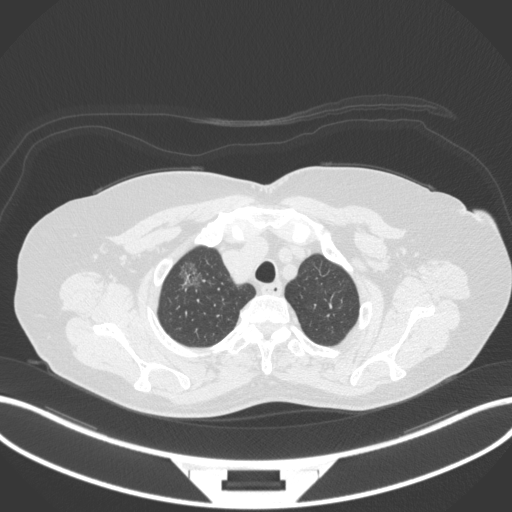
Chest CT, one axial slice; position 304 of 365 along the scan axis; reconstruction kernel B31f; lung window (W 1500 / L -600 HU); 1 mm slice thickness; 512 × 512 image matrix. Female patient, age 62 years. From the clinical record (not read from this slice): clinical TNM (as recorded): T1c N0 M0.
Structures marked on this image (bounding box drawn by a radiologist):
- lung tumour (recorded histology: adenocarcinoma): box from (x=173, y=259) to (x=211, y=298) px